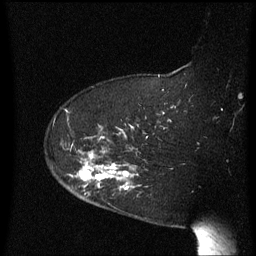
Breast MRI (dynamic contrast-enhanced), one sagittal slice. Position 48 of 60 along the scan axis. Dynamic contrast-enhanced series, image 2 of 3 at this slice position (ordered by acquisition). 1.5 T. TE 4.2 ms, TR 8.4 ms. 2.3 mm slice thickness. 256 × 256 image matrix. Female patient, age 63 years. From the clinical record (not read from this slice): setting: breast cancer imaged before/during neoadjuvant chemotherapy; receptor status: HER2-positive.
Outlined on this slice (semi-automatic segmentation, software-assisted and operator-edited):
- analysis volume of interest (the breast-tissue region the enhancement analysis was run in; not a lesion): box from (x=63, y=144) to (x=140, y=206) px
- tumour enhancement mask (voxels above the 70 % enhancement threshold inside the analysis volume of interest): (x=78, y=153)–(x=133, y=190)